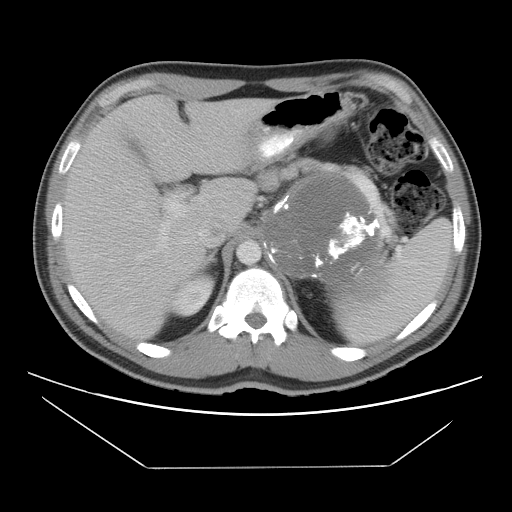
Contrast-enhanced abdominal CT, one axial slice; slice 75 of 131 in the series (ordered by position); 120 kVp; intravenous contrast given; soft-tissue window (W 400 / L 40 HU); 512 × 512 image matrix, field of view 396 × 396 mm. Patient: male, 44 years. From the clinical record (not read from this slice): diagnosis: adrenocortical carcinoma; tumour side: left adrenal; tumour size at pathology: 15.5 cm; Ki-67 index: 6 %; stage (as recorded): 2.
Structures marked on this image (semi-automatically segmented with operator editing):
- mass: box from (x=262, y=173) to (x=387, y=294) px